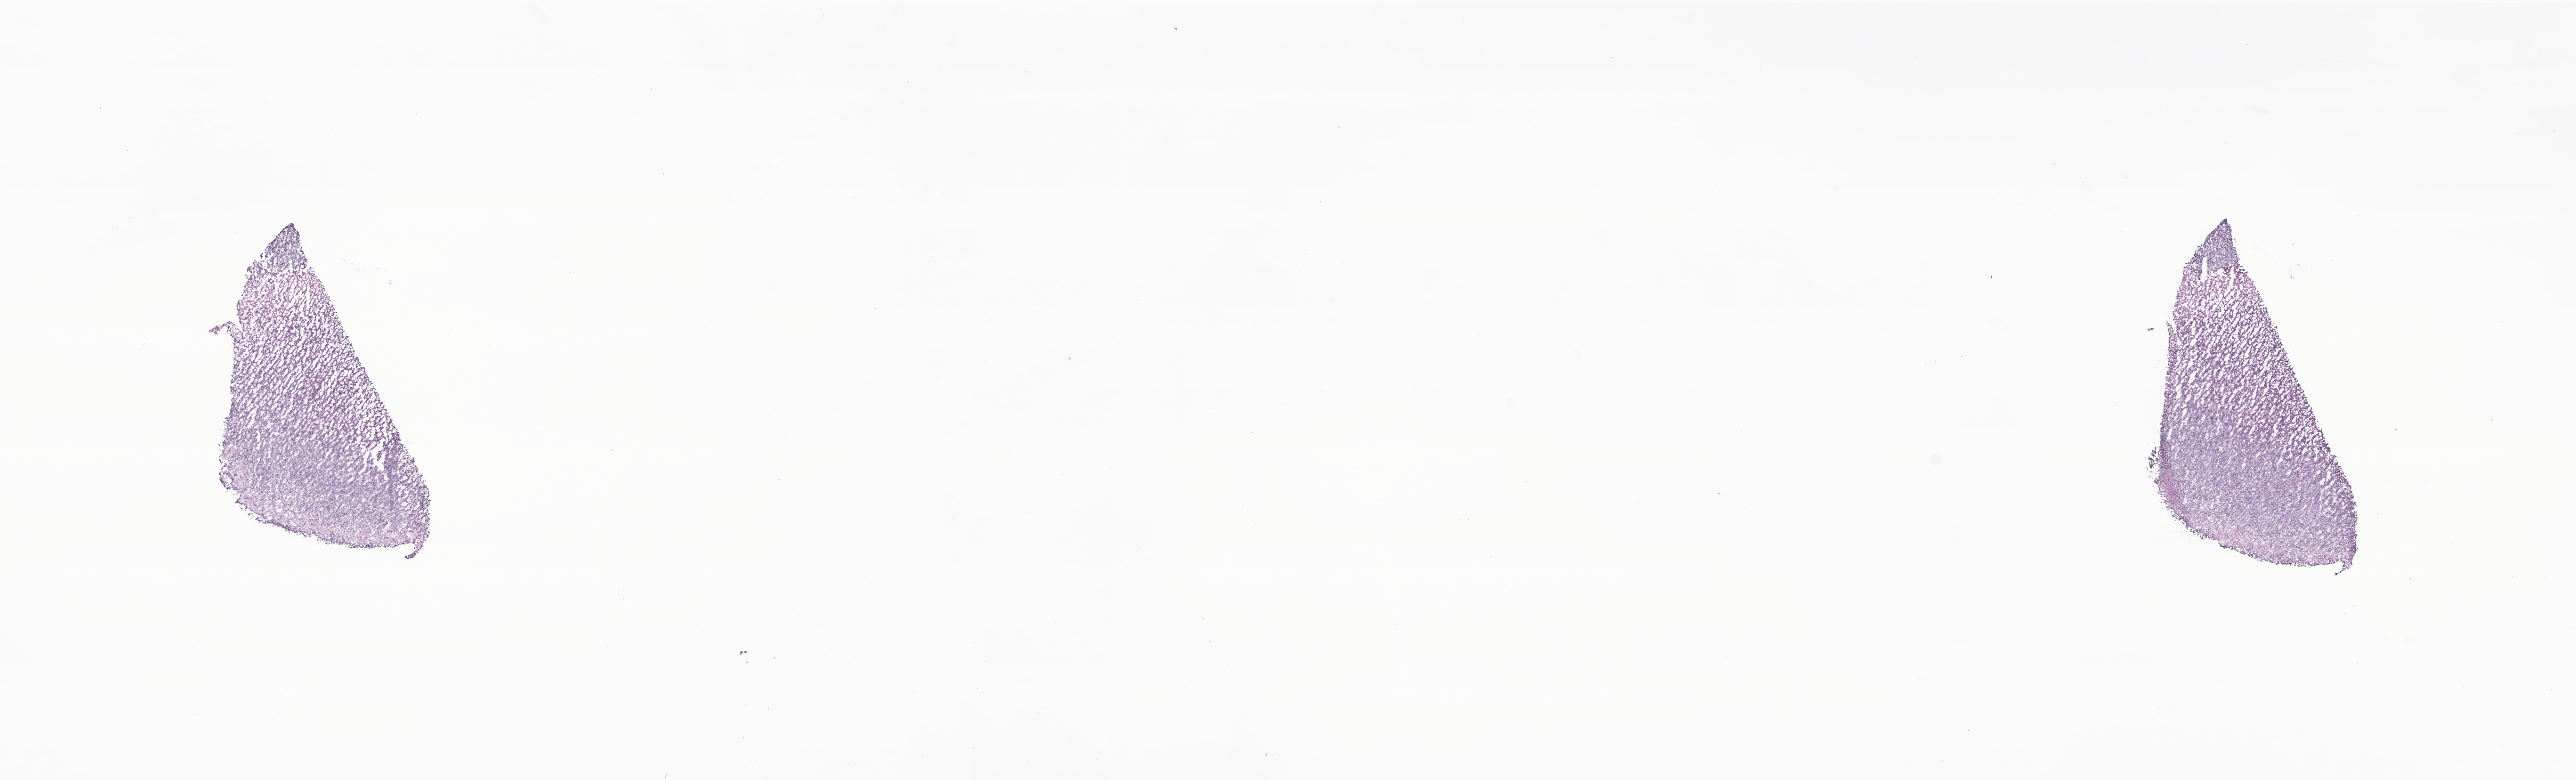
Digitized haematoxylin and eosin-stained section of tumor tissue from the cerebellum, whole scanned area (about 23.1 x 7.0 mm) shown as a low-resolution overview. Cryosection (OCT / tissue freezing medium). Patient: male, age 96 months (8 years).
Diagnosis: Medulloblastoma, NOS.